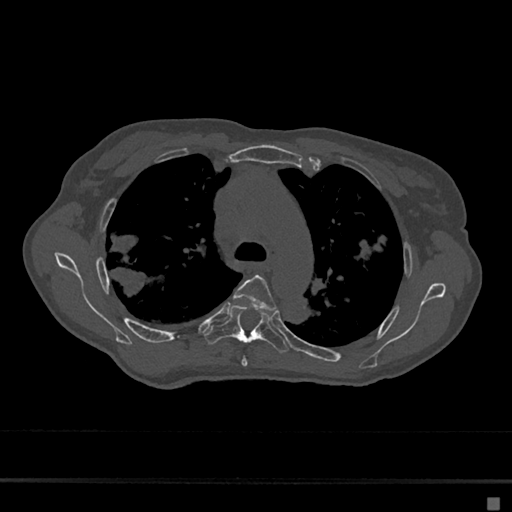
CT including the spine, one axial slice. Slice 477 of 797 in the series (ordered by position). Bone window (W 1800 / L 400 HU). 0.5 mm slice thickness. 512 × 512 image matrix. Female patient, age 68 years. Case-level facts recorded for this patient, not image findings: primary cancer: renal.
Annotated regions visible in this slice (semi-automatic segmentation, software-assisted and operator-edited):
- T4 vertebra: box from (x=234, y=275) to (x=277, y=367) px
- T5 vertebra: (x=205, y=304)–(x=289, y=353)